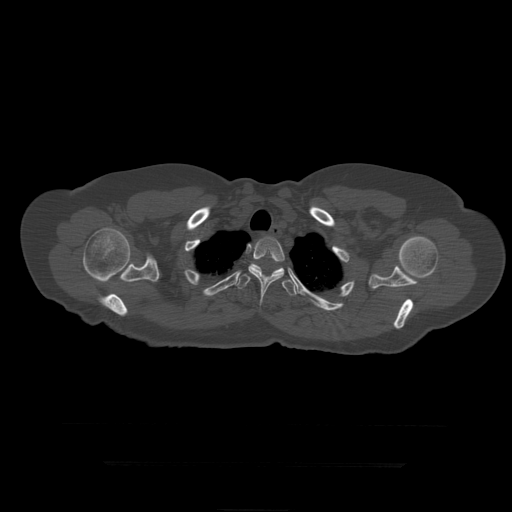
CT including the spine, one axial slice. Slice 359 of 399 in the series (ordered by position). 120 kVp. Bone window (W 1800 / L 400 HU). 1.25 mm slice thickness. 512 × 512 image matrix, field of view 450 × 450 mm. Patient age 41 years. Case-level facts recorded for this patient, not image findings: primary cancer: breast.
Structures marked on this image (semi-automatically segmented with operator editing):
- T3 vertebra: box from (x=249, y=237) to (x=285, y=306) px
- T4 vertebra: (x=235, y=264)–(x=297, y=296)